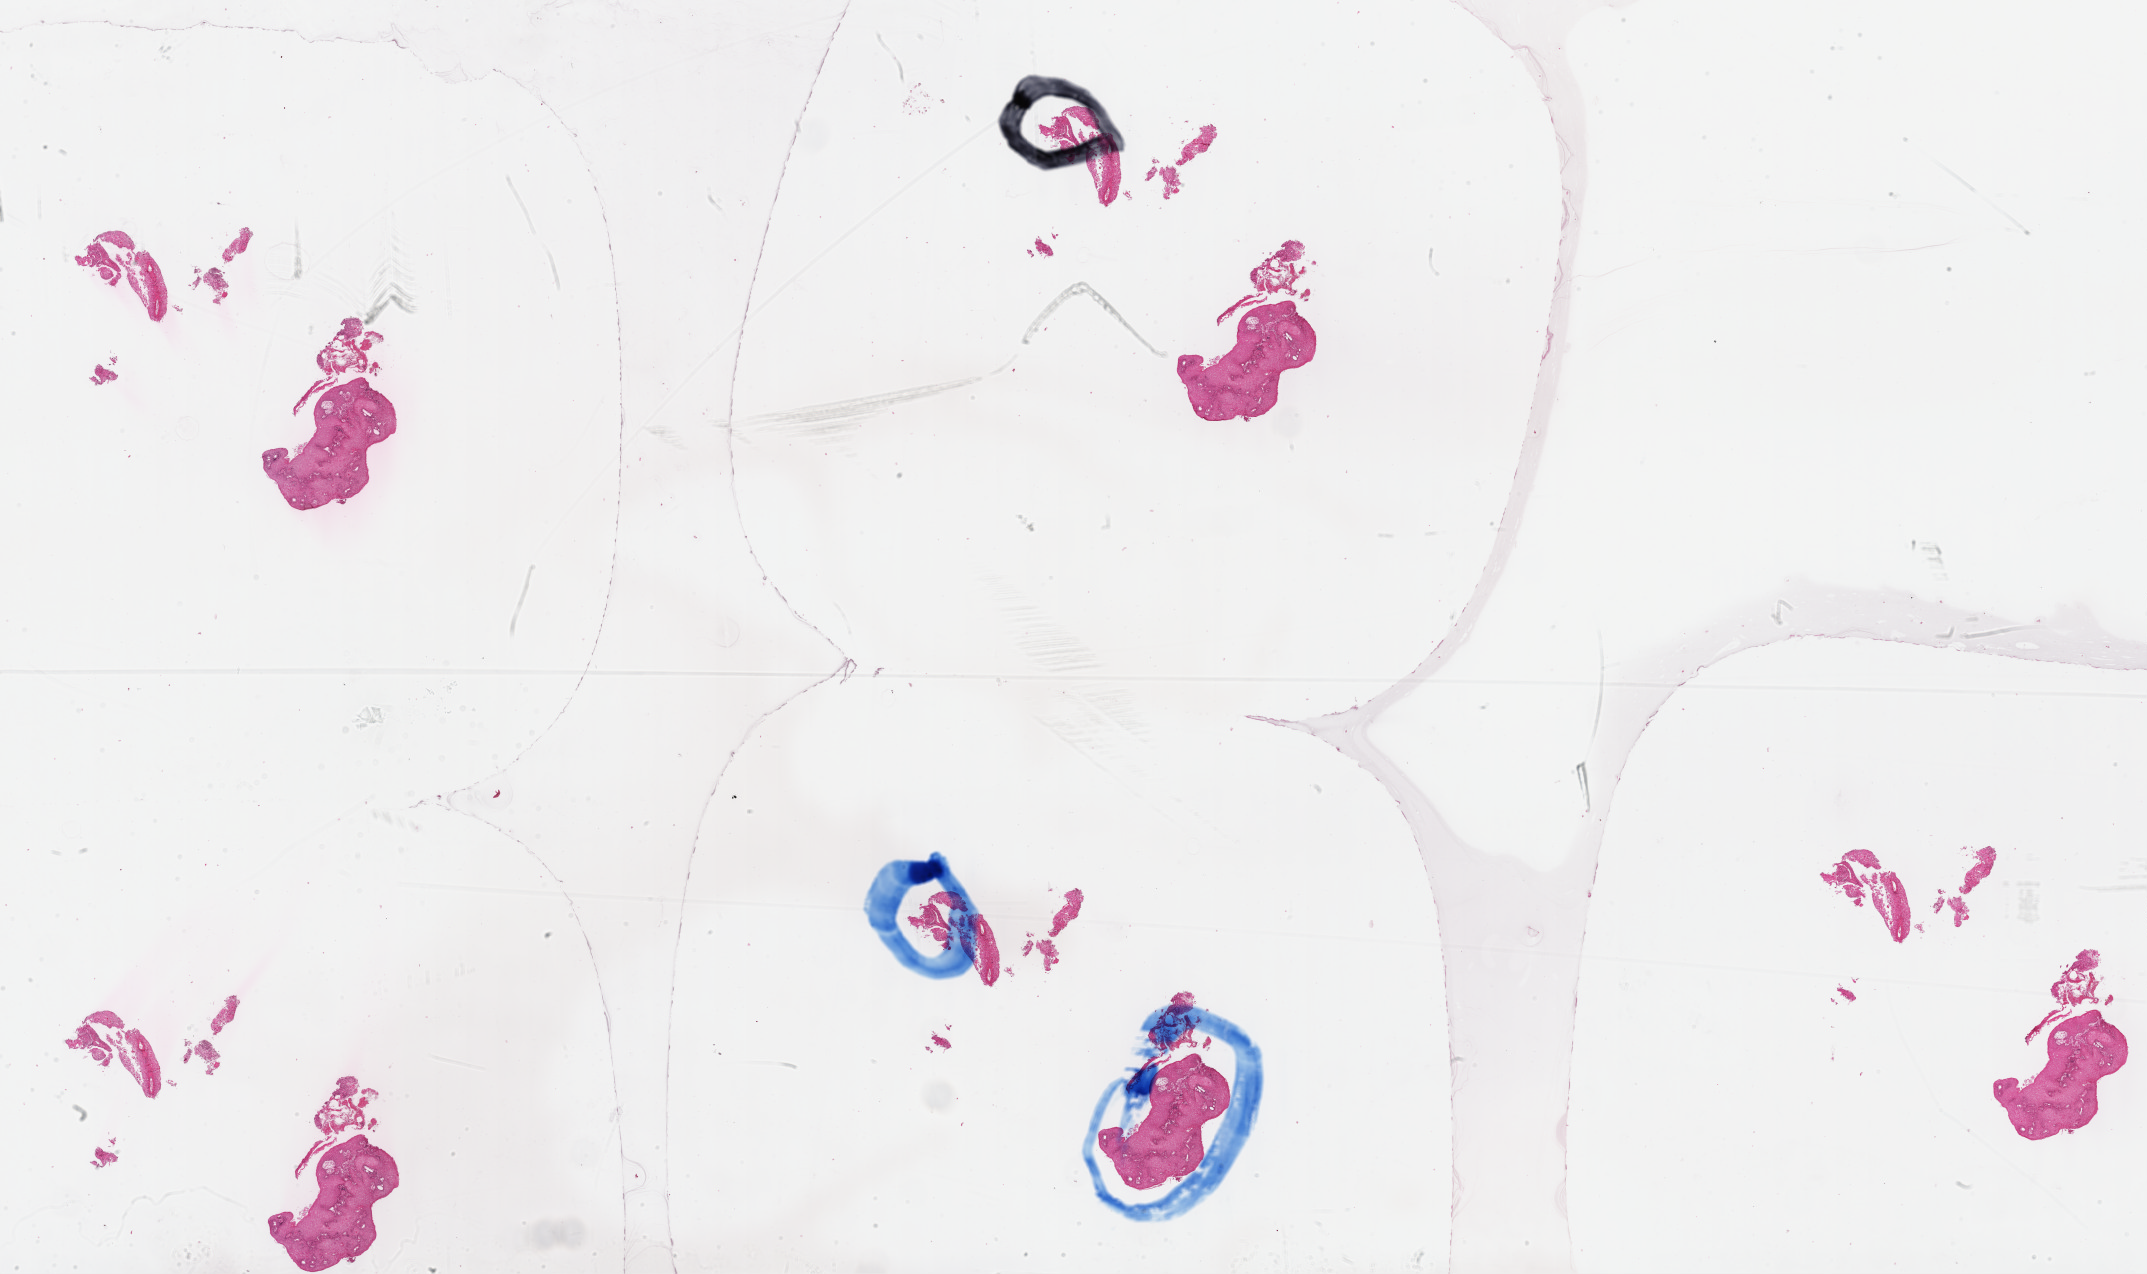
H&E-stained whole-slide image — whole scanned area (about 34.7 x 20.6 mm, acquisition: 40x scan) shown as a low-resolution overview. Formalin-fixed paraffin-embedded (FFPE) diagnostic section. Head and neck, primary tumour sample. Female patient; age at initial diagnosis 43 years. Histologic grade: G2 (moderately differentiated).
• pathologic diagnosis: Squamous cell carcinoma, NOS (tongue, NOS)
• lymph nodes positive (case pathology): 1 of 24 examined
• laterality: right